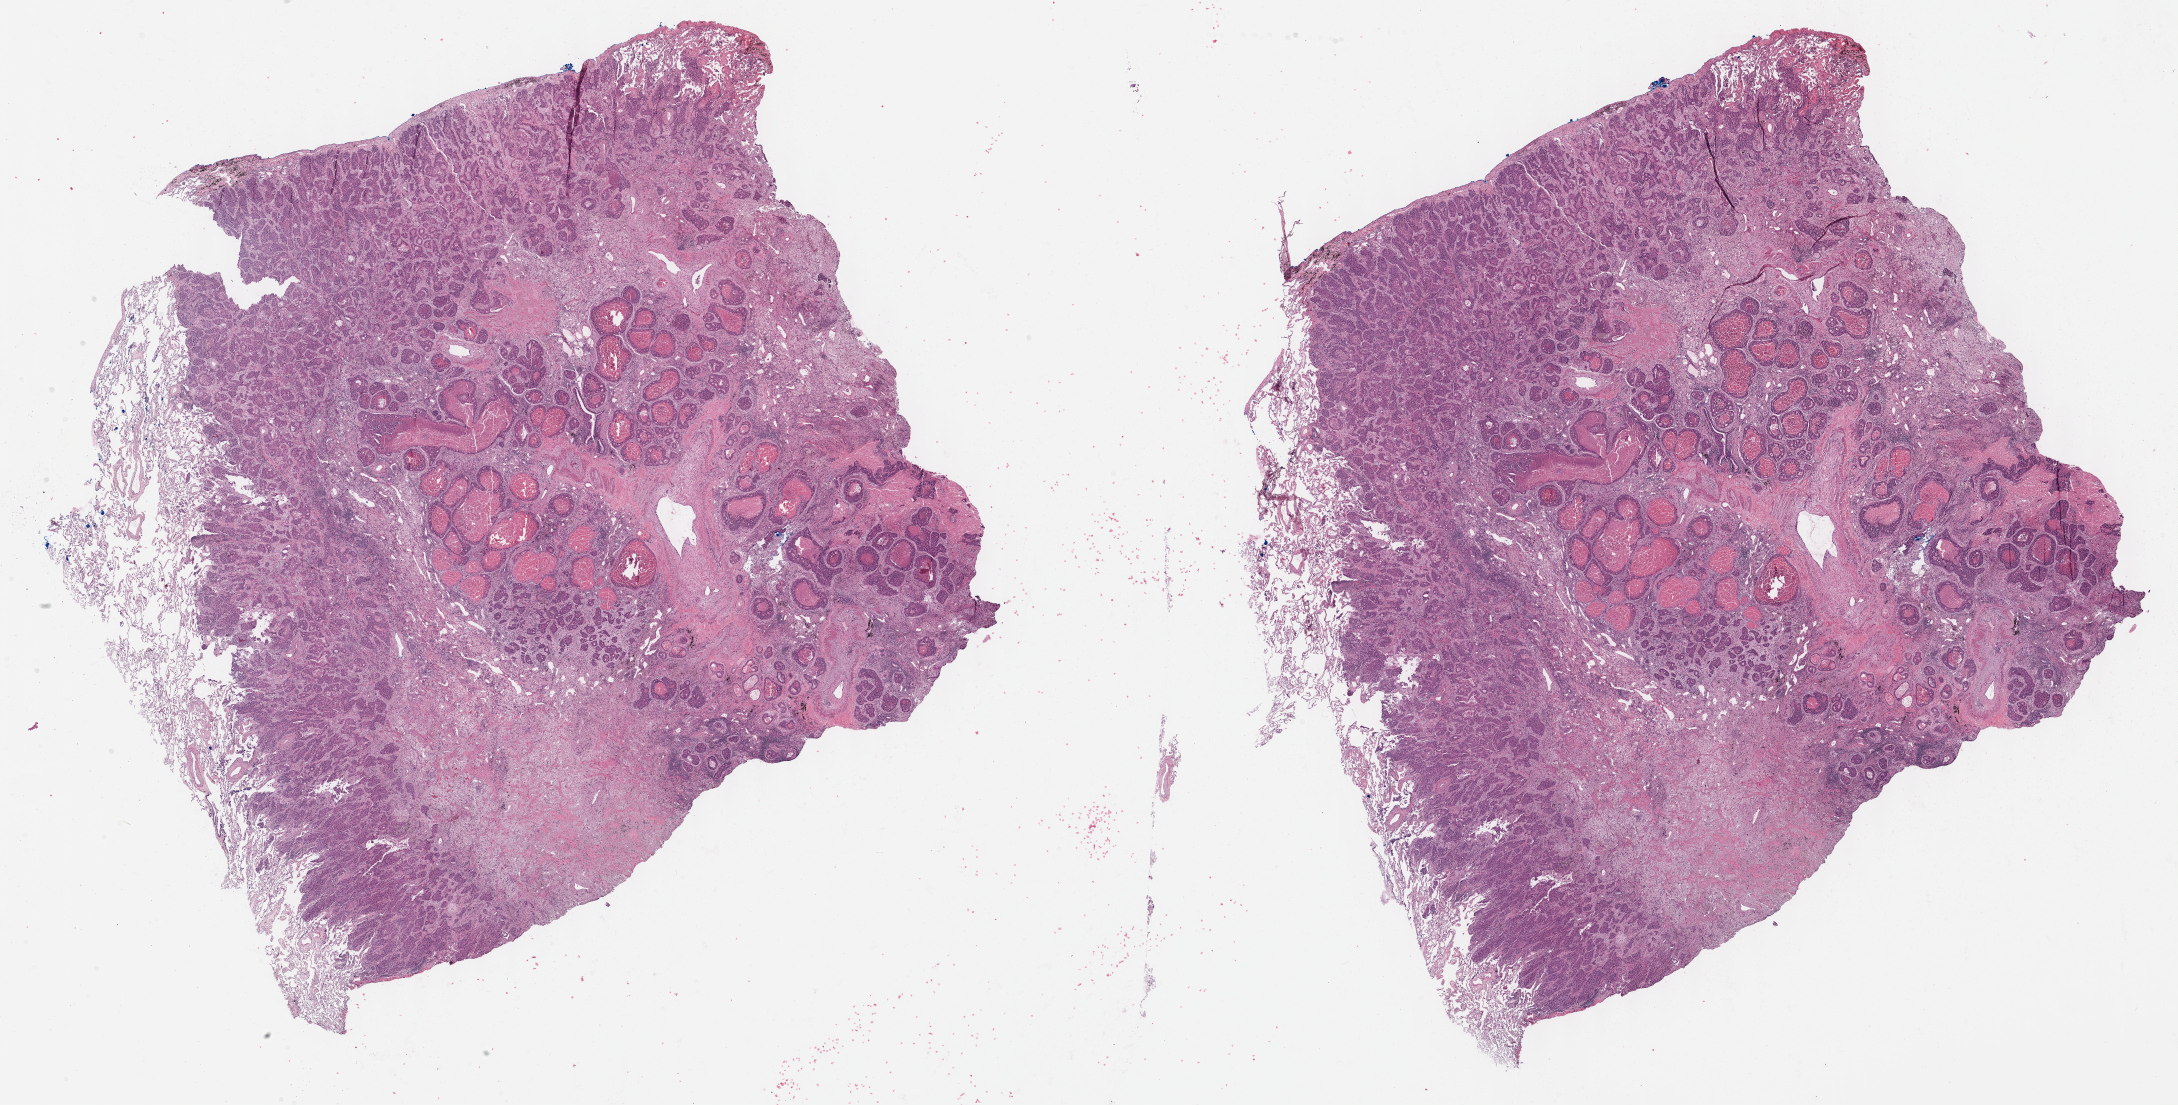
Whole-slide histology image, H&E, low-resolution overview of the scanned area, about 35.2 x 17.9 mm (from a 40x scan). Formalin-fixed paraffin-embedded (FFPE) diagnostic section. Sample: primary tumour, lung. Patient: male, age at initial diagnosis 67 years.
Histologic diagnosis: Solid carcinoma, NOS (upper lobe, lung).